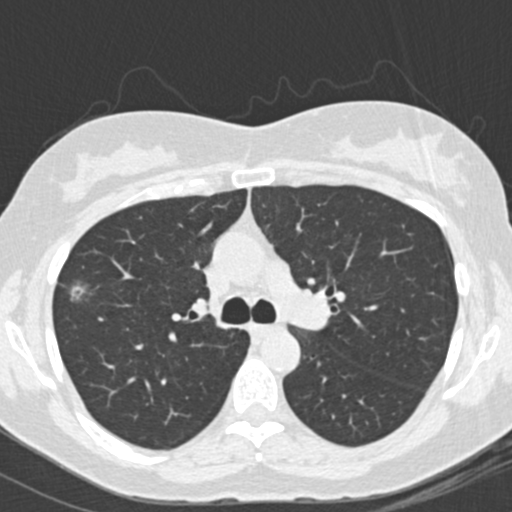
Low-dose screening chest CT, one axial slice; slice 107 of 157 in the series (ordered by position); reconstruction kernel B30f; lung window (W 1500 / L -600 HU); 2 mm slice thickness; 512 × 512 image matrix, field of view 290 × 290 mm.
Outlined on this slice (expert manual segmentation):
- lesion 1 (tumor, upper lobe of right lung): bounding box (x1, y1, x2, y2) in pixels: (71, 286, 85, 300)